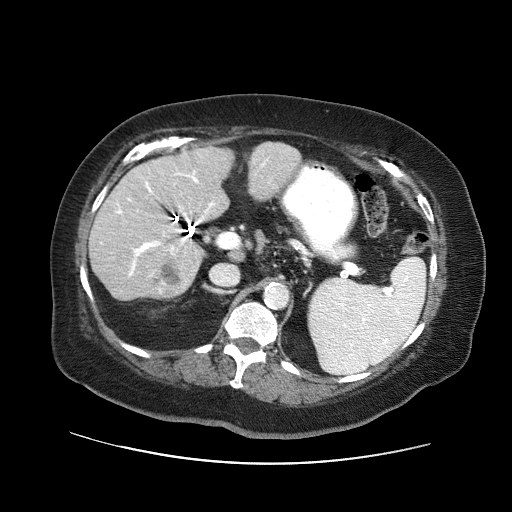
Contrast-enhanced abdominal CT (liver protocol), one axial slice. Position 25 of 71 along the scan axis. Reconstruction kernel STANDARD. 120 kVp. Soft-tissue window (W 400 / L 40 HU). 2.5 mm slice thickness. 512 × 512 image matrix. Case-level facts recorded for this patient, not image findings: diagnosis: hepatocellular carcinoma (patient treated with transarterial chemoembolisation; whether this scan precedes or follows treatment is not stated here); TNM stage (as recorded): Stage-II; Child-Pugh class: A; tumour differentiation: poorly differentiated; tumour nodularity: multinodular.
Outlined on this slice (semi-automatic segmentation, software-assisted and operator-edited):
- liver parenchyma outside the tumour (the mass and vessels are separate outlines, so this box may not span the whole liver): bounding box [x1, y1, x2, y2] px = [88, 142, 301, 298]
- mass: [149, 256, 182, 296]
- liver vessels: [101, 159, 268, 276]